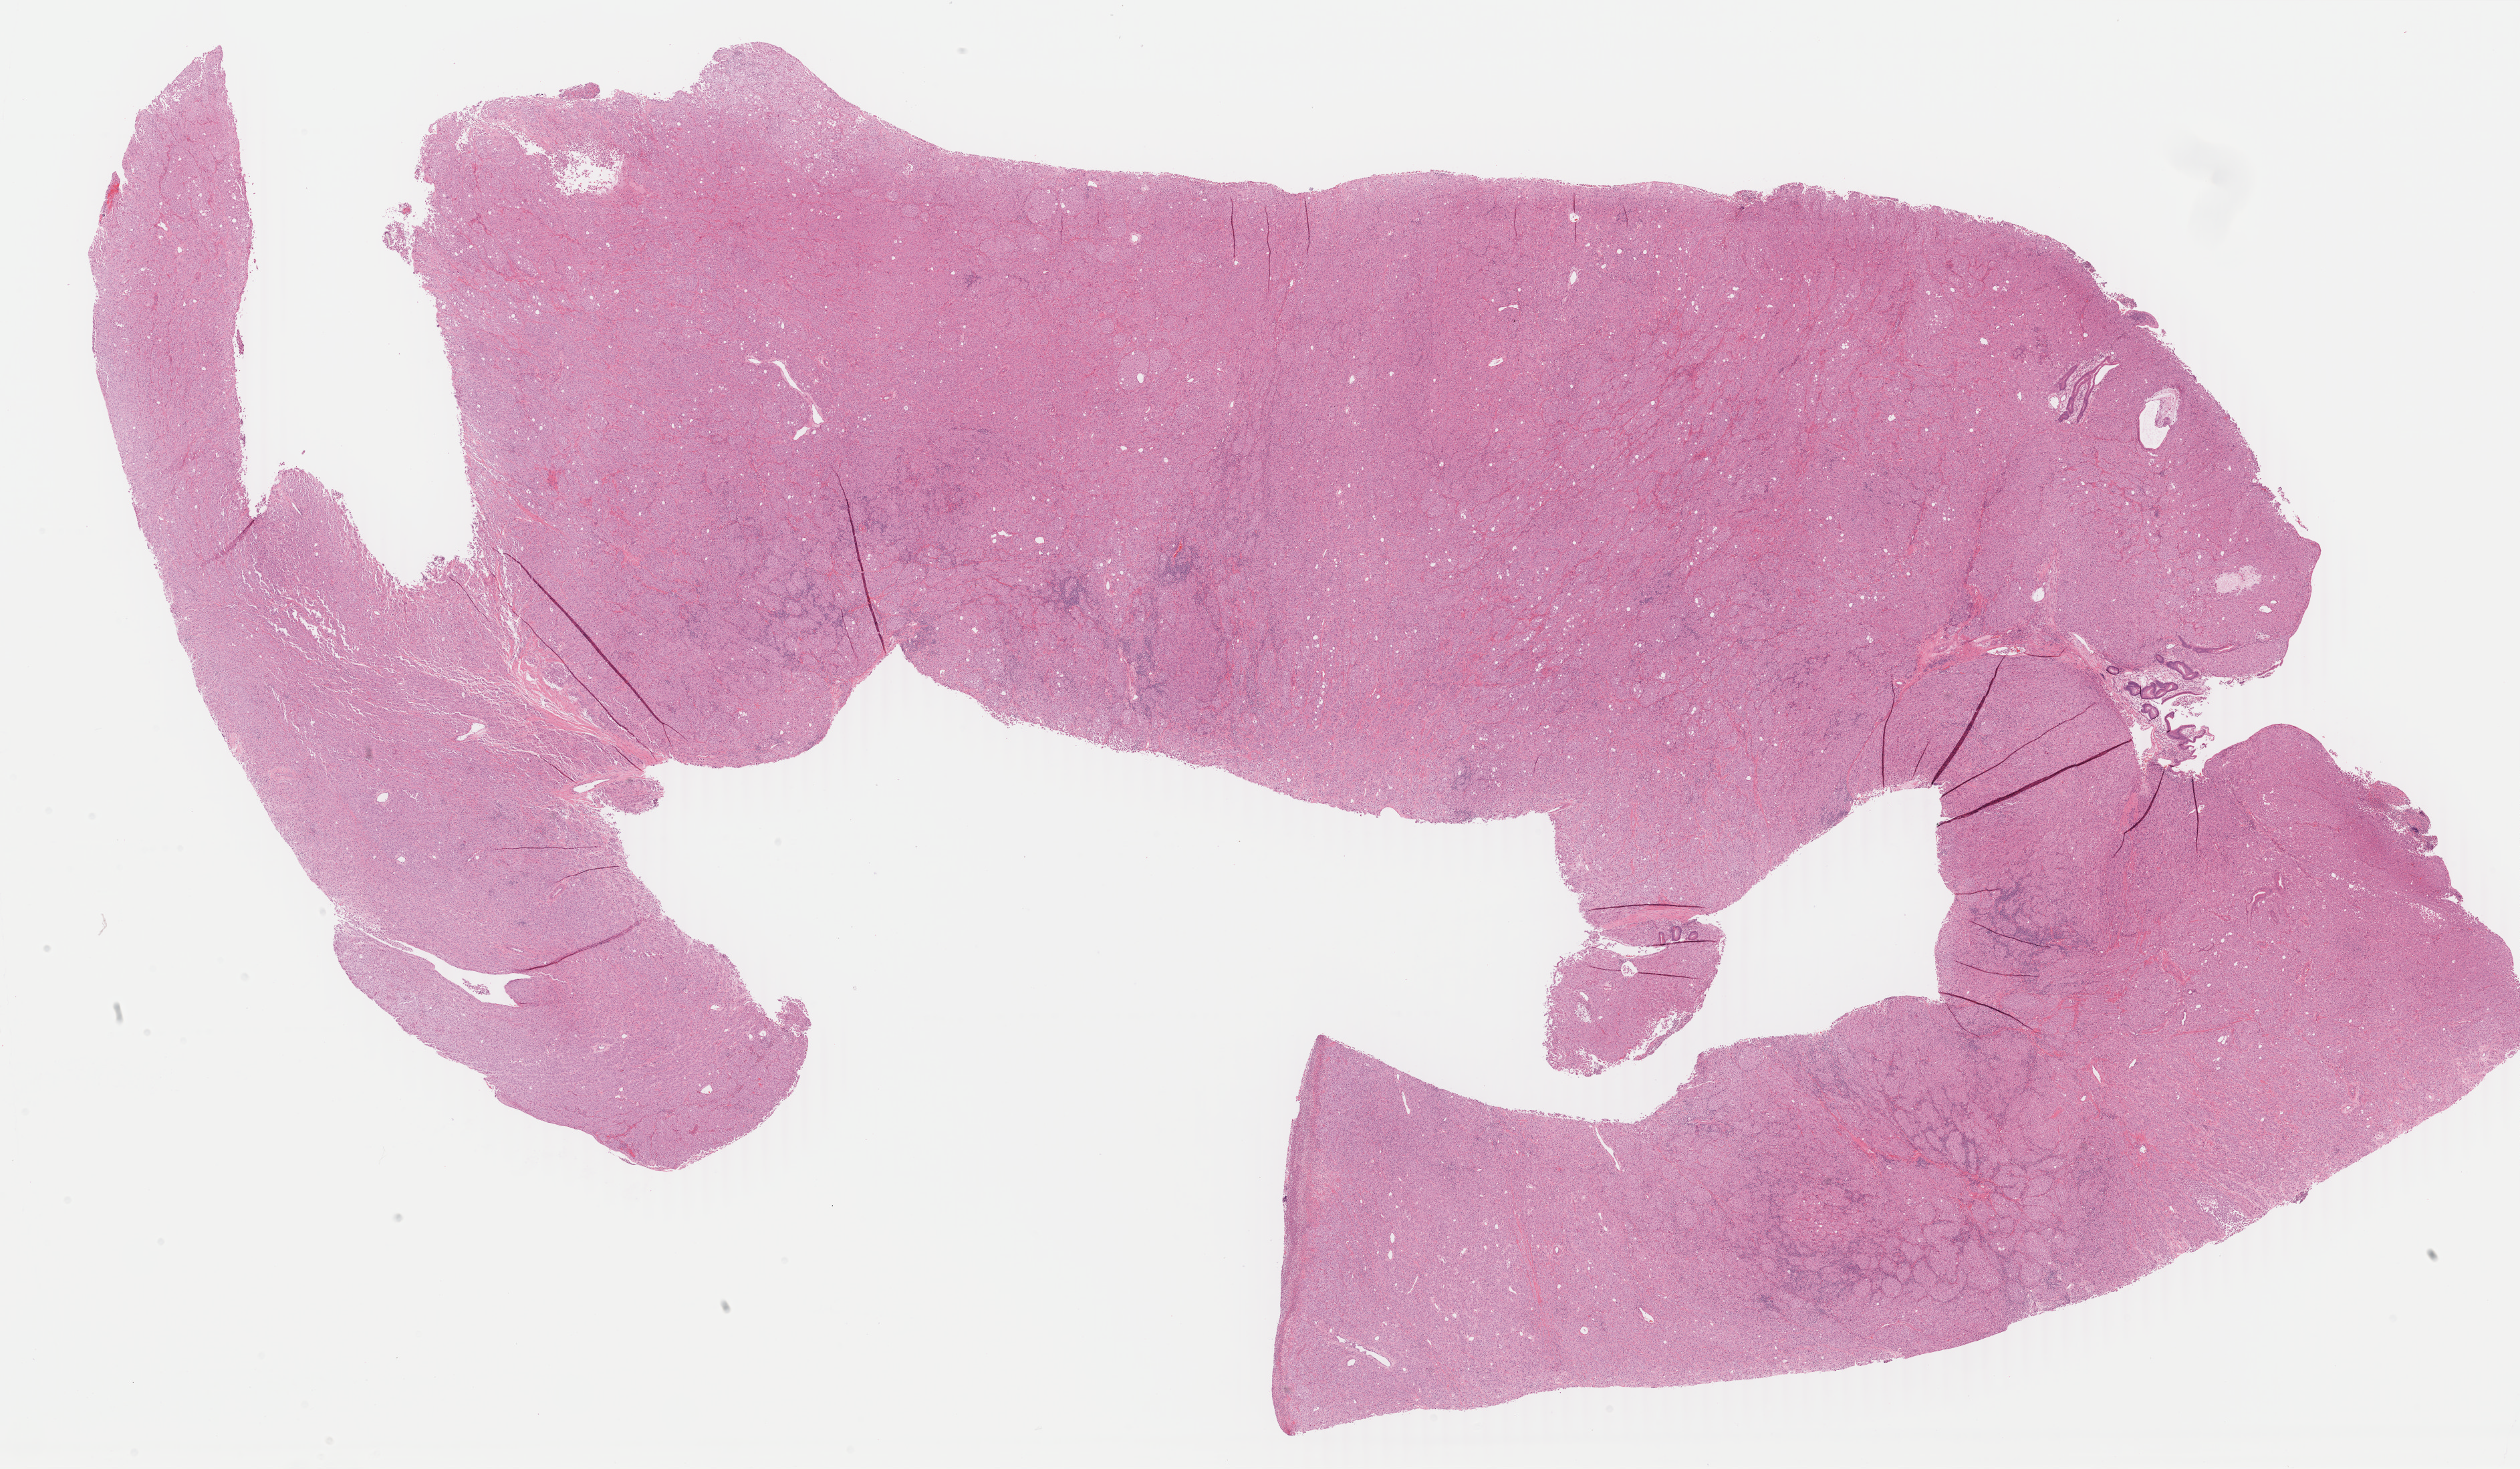
Whole-slide histology image, H&E, shown as a low-resolution overview of the whole scanned area (about 30.0 x 17.5 mm, acquisition: 40x scan), formalin-fixed paraffin-embedded (FFPE) diagnostic section, metastatic tumour sample, sampled site not recorded. Male patient; age at initial diagnosis 49 years.
This section: metastatic tumour tissue. Patient diagnosis: Malignant melanoma, NOS.